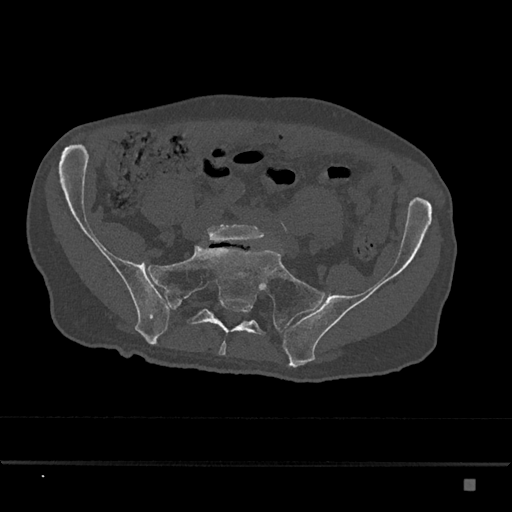
CT including the spine, one axial slice. Slice 215 of 797 in the series (ordered by position). Reconstruction kernel Br40s/3. 120 kVp. Bone window (W 1800 / L 400 HU). 0.5 mm slice thickness. 512 × 512 image matrix, field of view 390 × 390 mm. Male patient, age 72 years. From the clinical record (not read from this slice): primary cancer: prostate.
Outlined on this slice (semi-automatic segmentation, software-assisted and operator-edited):
- L5 vertebra: bounding box <207,224,265,242> (left, top, right, bottom; pixels)